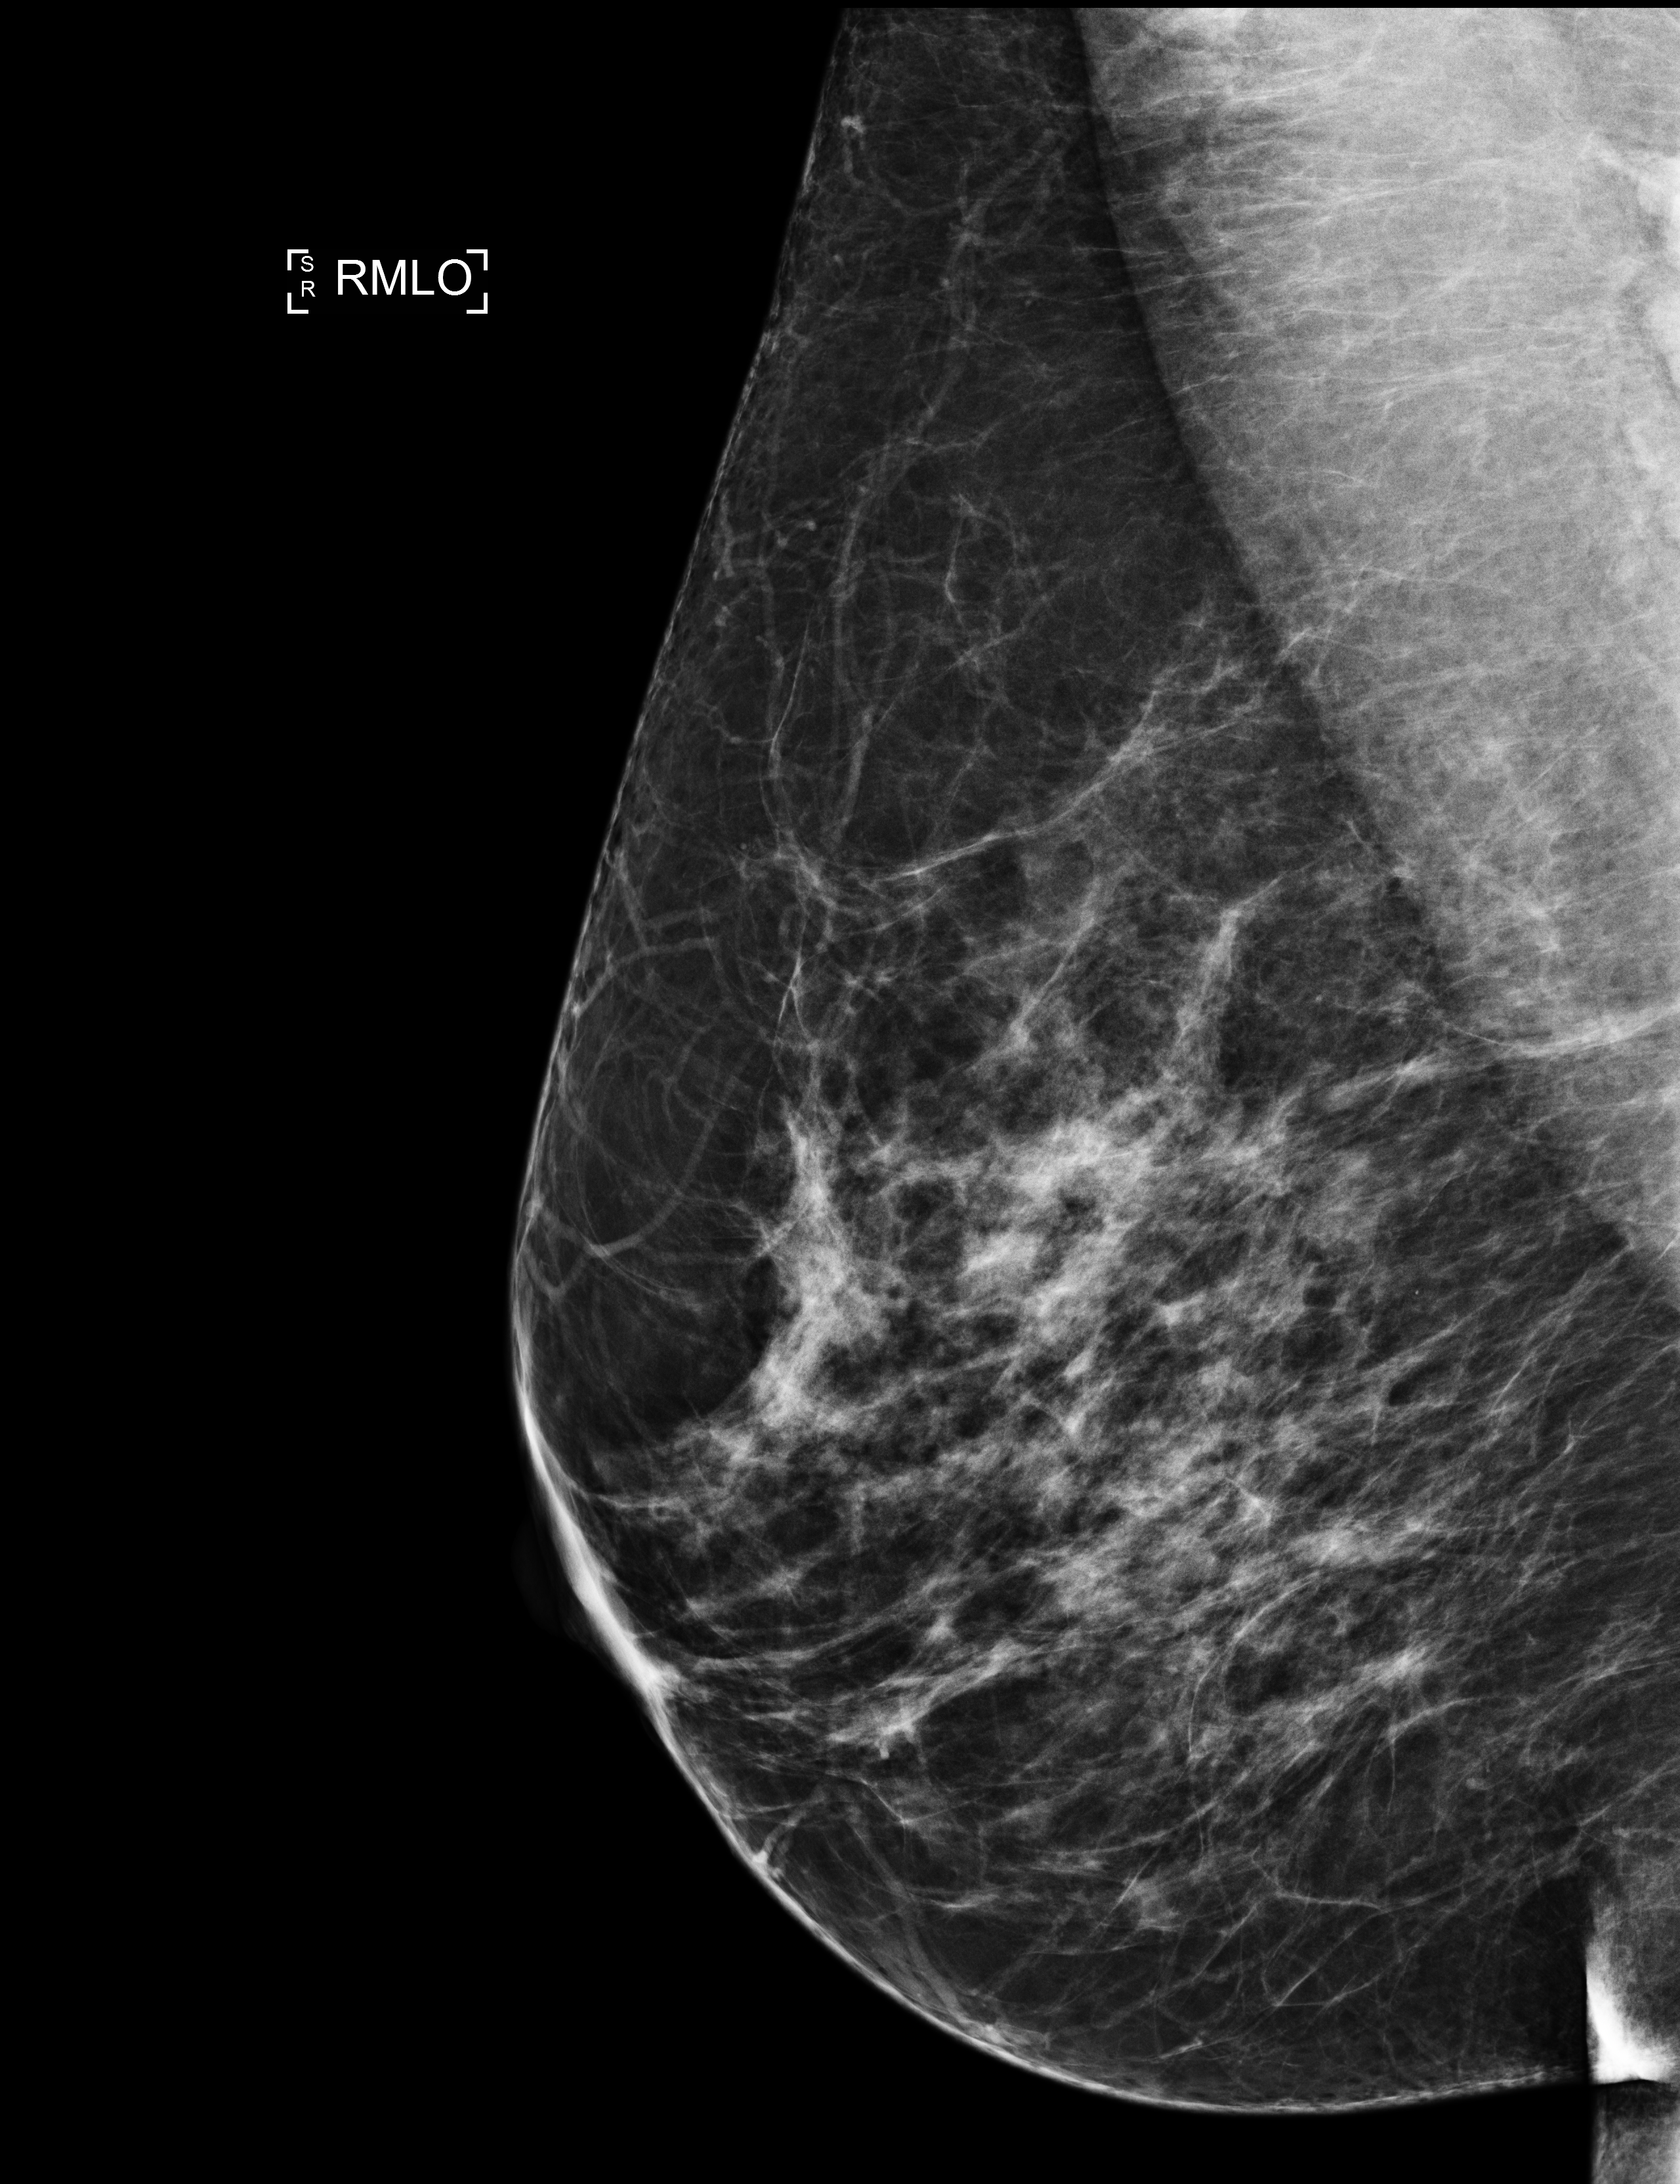
Full-field digital mammogram (FFDM); right breast; mediolateral oblique (MLO) view; screening examination. Female patient, age 50 years.
BI-RADS breast density category at the screening exam (both breasts, scale 1–4): 3. Final BI-RADS assessment for this screening round (tomosynthesis exam, both breasts): category 1. Recall: no recall after this screen.